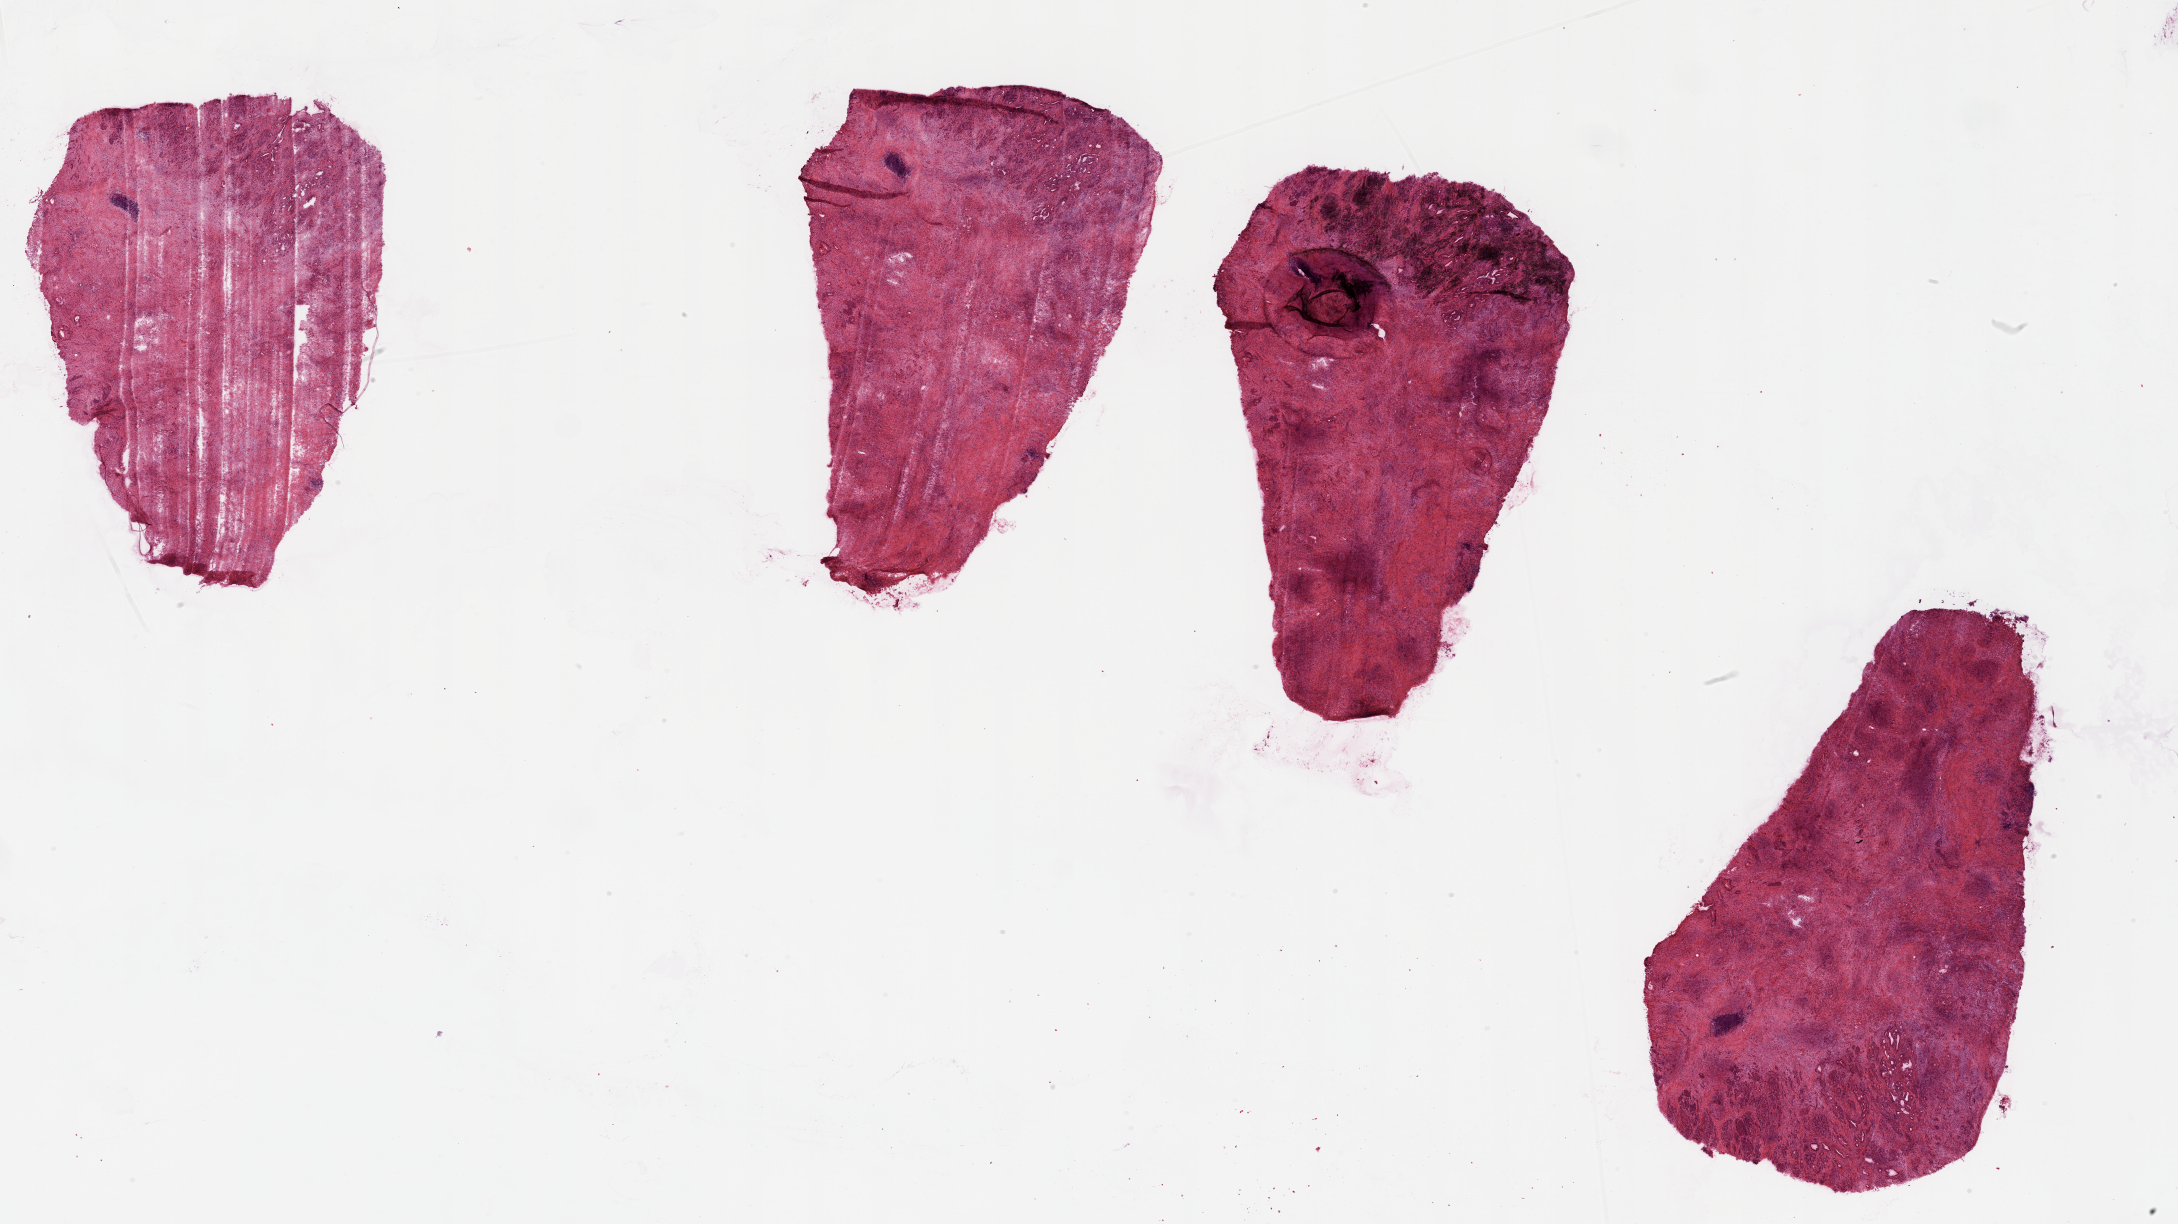
Digitized H&E tissue section (whole slide), a low-resolution overview of the entire scanned area, about 34.5 x 19.4 mm (acquisition: 20x scan), pancreas, tumour tissue. Patient: male, age 65 years. Histologic grade: G3 (poorly differentiated).
Histologic diagnosis: Infiltrating duct carcinoma, NOS. Primary tumour site (as recorded): head. AJCC pathologic stage: III.